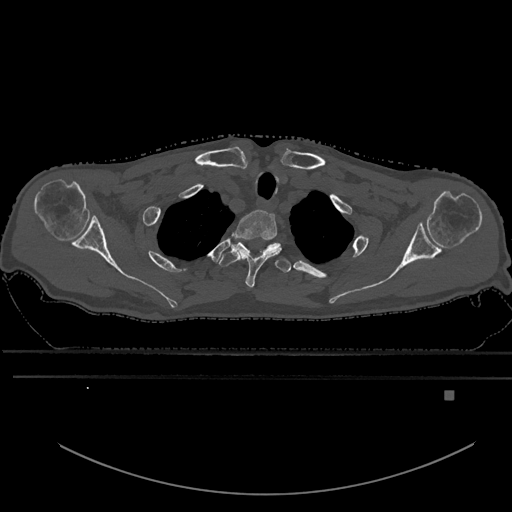
CT including the spine, one axial slice; position 518 of 969 along the scan axis; bone window (W 1800 / L 400 HU); 512 × 512 image matrix, field of view 456 × 456 mm. Male patient, age 82 years. Case-level facts recorded for this patient, not image findings: primary cancer: prostate; vertebrae with lytic lesions (as recorded): T11, T9, T8, T2.
Annotated regions visible in this slice (semi-automatic segmentation, software-assisted and operator-edited):
- T1 vertebra: bounding box (x1, y1, x2, y2) in pixels: (235, 209, 279, 291)
- T2 vertebra: (219, 239, 280, 267)